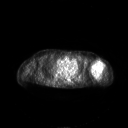
FDG PET of an extremity soft-tissue mass (from a PET/CT study), one axial slice. Slice 171 of 267 in the series (ordered by position). 3.27 mm slice thickness. 128 × 128 image matrix, field of view 700 × 700 mm. Female patient, age 83 years. From the clinical record (not read from this slice): histological type: pleiomorphic leiomyosarcoma; grade: high; site of the primary tumour: left biceps.
Annotated regions visible in this slice (expert contour drawn on MRI and transferred to this co-registered scan by the dataset authors):
- gross tumour volume including surrounding oedema: bounding box <90,59,105,77> (left, top, right, bottom; pixels)
- gross tumour volume (mass): <90,59,103,76>